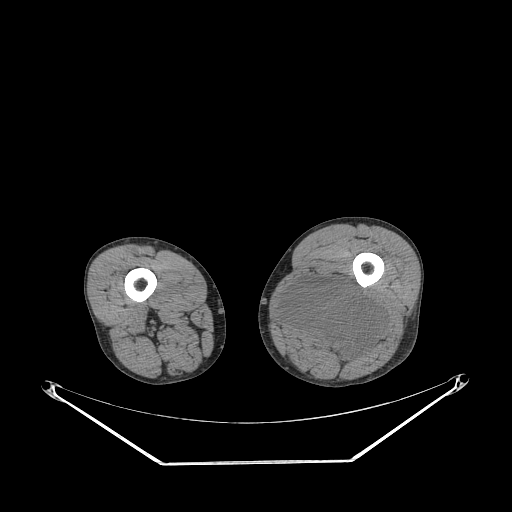
CT of an extremity soft-tissue mass (from a PET/CT study), one axial slice. Position 223 of 267 along the scan axis. 140 kVp. Soft-tissue window (W 400 / L 40 HU). 3.75 mm slice thickness. 512 × 512 image matrix, field of view 500 × 500 mm. Male patient. From the clinical record (not read from this slice): histological type: undifferentiated pleomorphic liposarcoma; grade: high; site of the primary tumour: left thigh.
Structures marked on this image (expert contour drawn on MRI and transferred to this co-registered scan by the dataset authors):
- gross tumour volume including surrounding oedema: bounding box <279,278,385,360> (left, top, right, bottom; pixels)
- gross tumour volume (mass): <281,278,385,360>